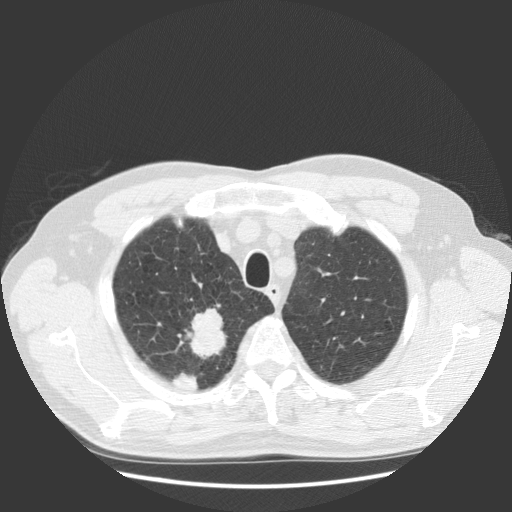
Low-dose screening chest CT, one axial slice; position 106 of 131 along the scan axis; reconstruction kernel STANDARD; 140 kVp; lung window (W 1500 / L -600 HU); 512 × 512 image matrix, field of view 369 × 369 mm.
Structures marked on this image (expert manual segmentation):
- lesion 1 (tumor, upper lobe of right lung): bounding box [x1, y1, x2, y2] px = [184, 308, 227, 359]
- lesion 2 (tumor, upper lobe of right lung): [173, 373, 199, 391]